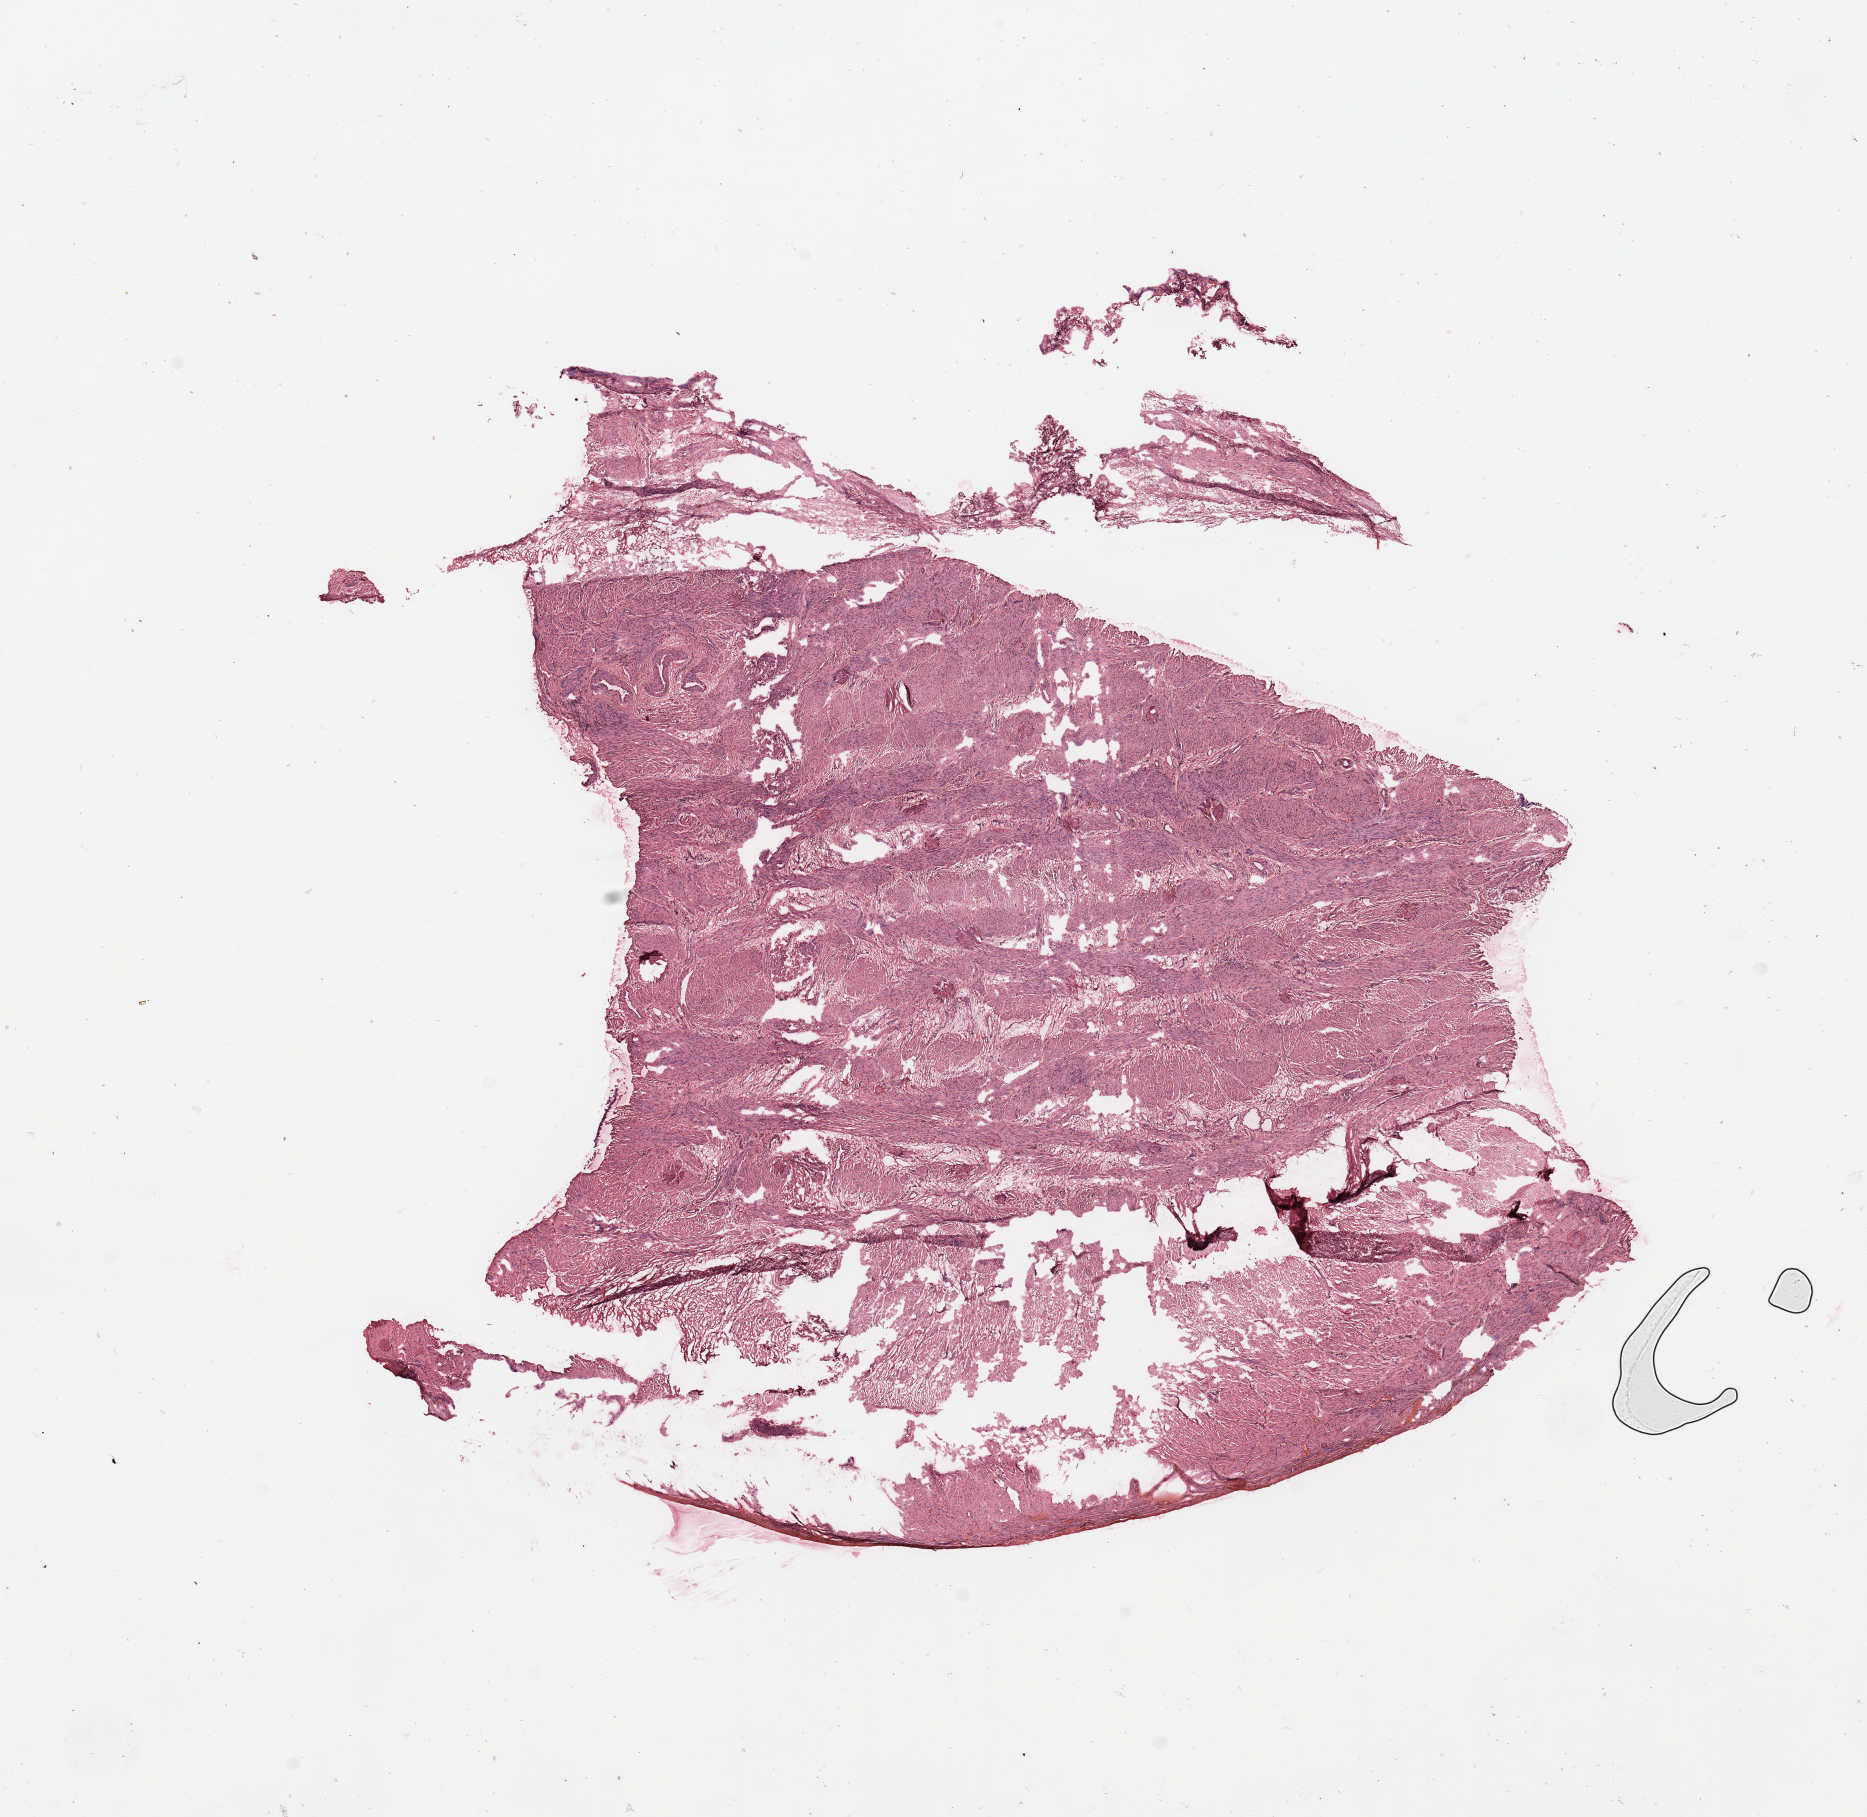
Digitized H&E tissue section (whole slide), whole scanned area (about 14.8 x 14.4 mm) shown as a low-resolution overview. Uterus, normal (non-tumour) tissue. 45-year-old female patient.
This section: normal (non-tumour) tissue from the same patient. Patient diagnosis: Endometrioid adenocarcinoma, NOS.